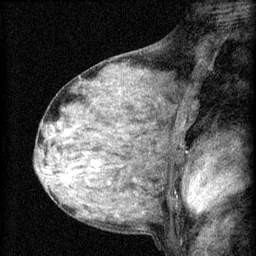
Breast MRI (dynamic contrast-enhanced), one sagittal slice. Position 37 of 60 along the scan axis. 3 images stored at this slice position (order not interpretable as contrast timing). 1.5 T. TE 4.2 ms, TR 8.2 ms. 2 mm slice thickness. 256 × 256 image matrix, field of view 180 × 180 mm. Patient: female, 48 years.
Structures marked on this image (semi-automatically segmented with operator editing):
- analysis volume of interest (the breast-tissue region the enhancement analysis was run in; not a lesion): bounding box <54,138,133,191> (left, top, right, bottom; pixels)
- tumour enhancement mask (voxels above the 70 % enhancement threshold inside the analysis volume of interest): <68,160,97,171>